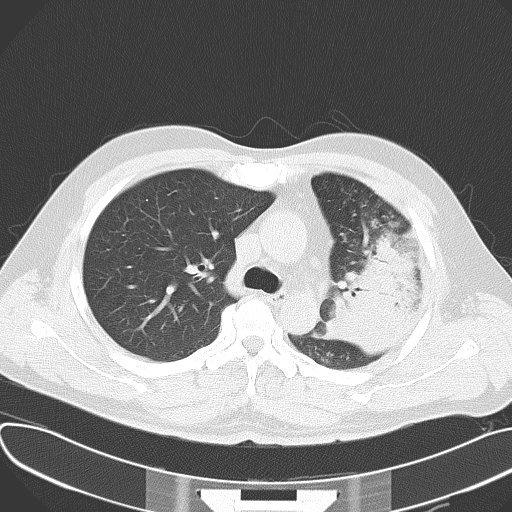
Chest CT, one axial slice. Slice 43 of 62 in the series (ordered by position). Reconstruction kernel B70f. Lung window (W 1500 / L -600 HU). 512 × 512 image matrix, field of view 377 × 377 mm. Male patient, age 48 years. Case-level facts recorded for this patient, not image findings: clinical TNM (as recorded): T4 N0 M0.
Outlined on this slice (bounding box drawn by a radiologist):
- lung tumour (recorded histology: adenocarcinoma): bounding box (x1, y1, x2, y2) in pixels: (328, 233, 420, 360)